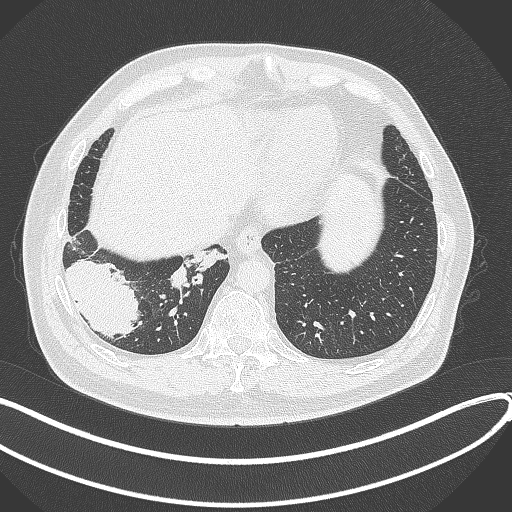
Chest CT, one axial slice. Position 74 of 360 along the scan axis. Reconstruction kernel B70f. 120 kVp. Lung window (W 1500 / L -600 HU). 512 × 512 image matrix, field of view 400 × 400 mm. Patient: male, 59 years.
Structures marked on this image (rectangle marked by the reading radiologist):
- lung tumour (recorded histology: adenocarcinoma): box from (x=64, y=257) to (x=145, y=338) px